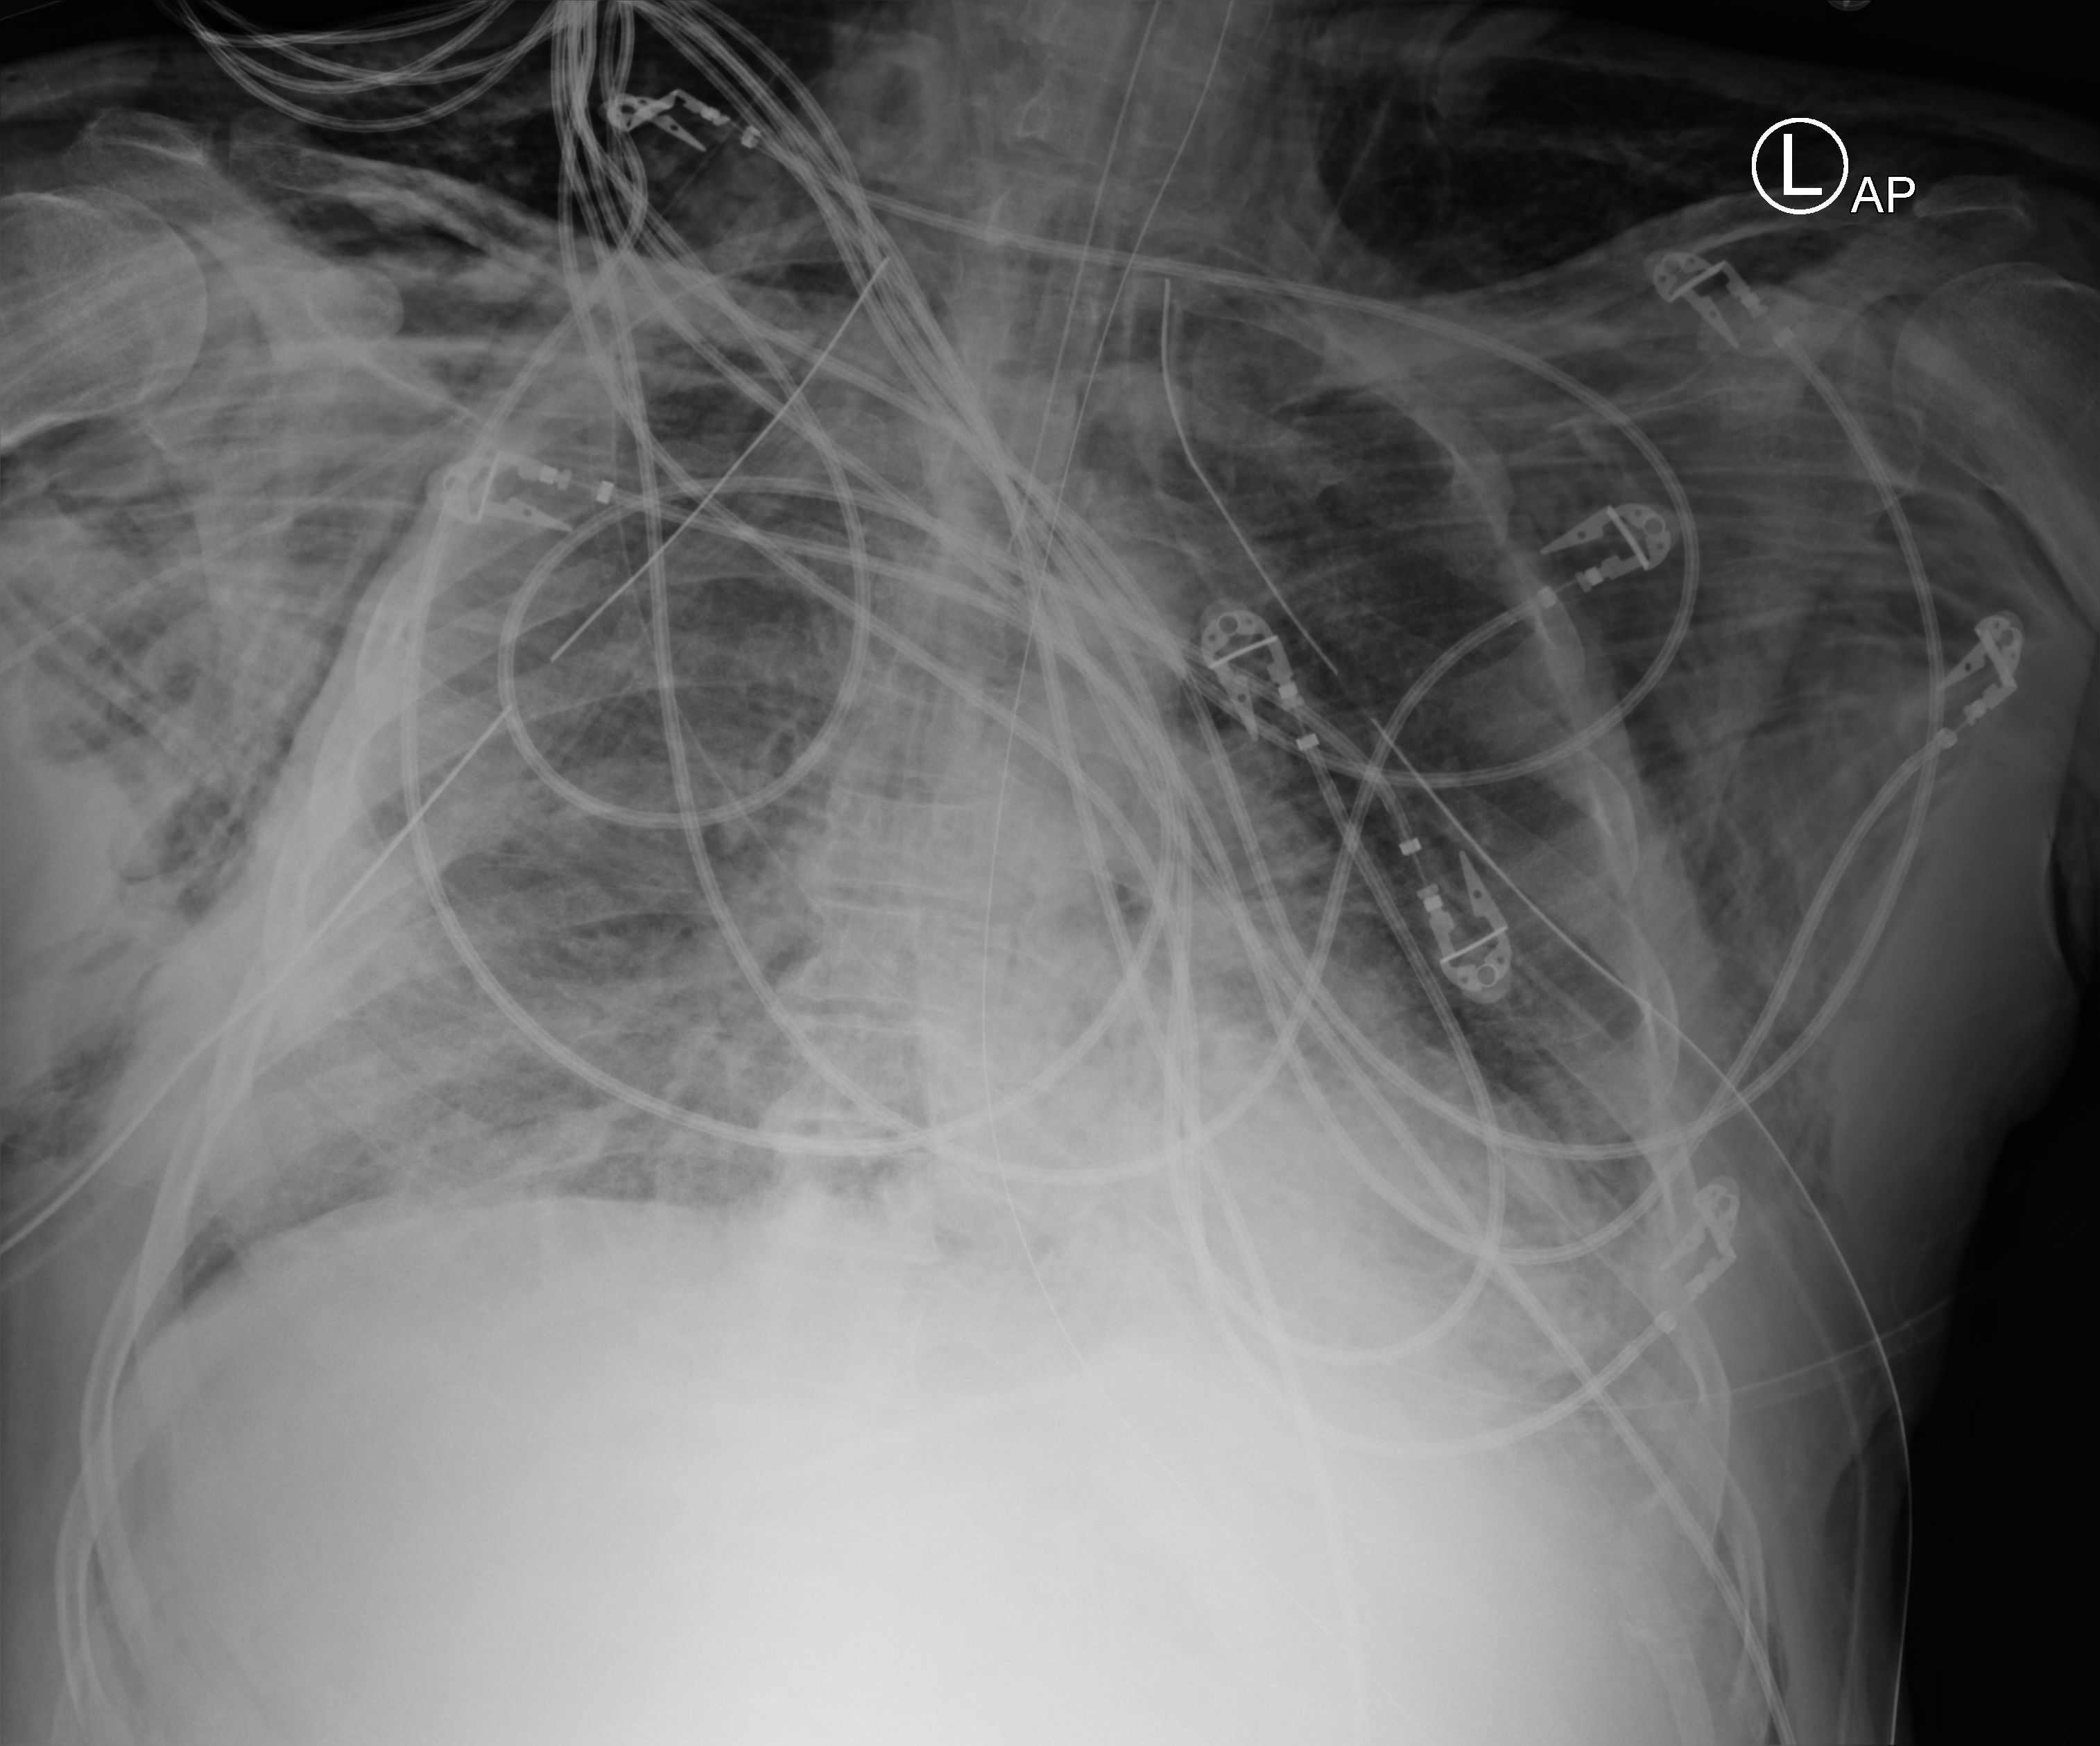
Chest X-ray (portable), anteroposterior (AP) projection. Male patient hospitalised with COVID-19, age 18–59 years.
From the hospital-stay record, not from the radiograph (when in the stay this image was taken is not recorded): smoking status (admission record): never; mechanically ventilated during this hospital stay: yes; COPD (admission record): no.